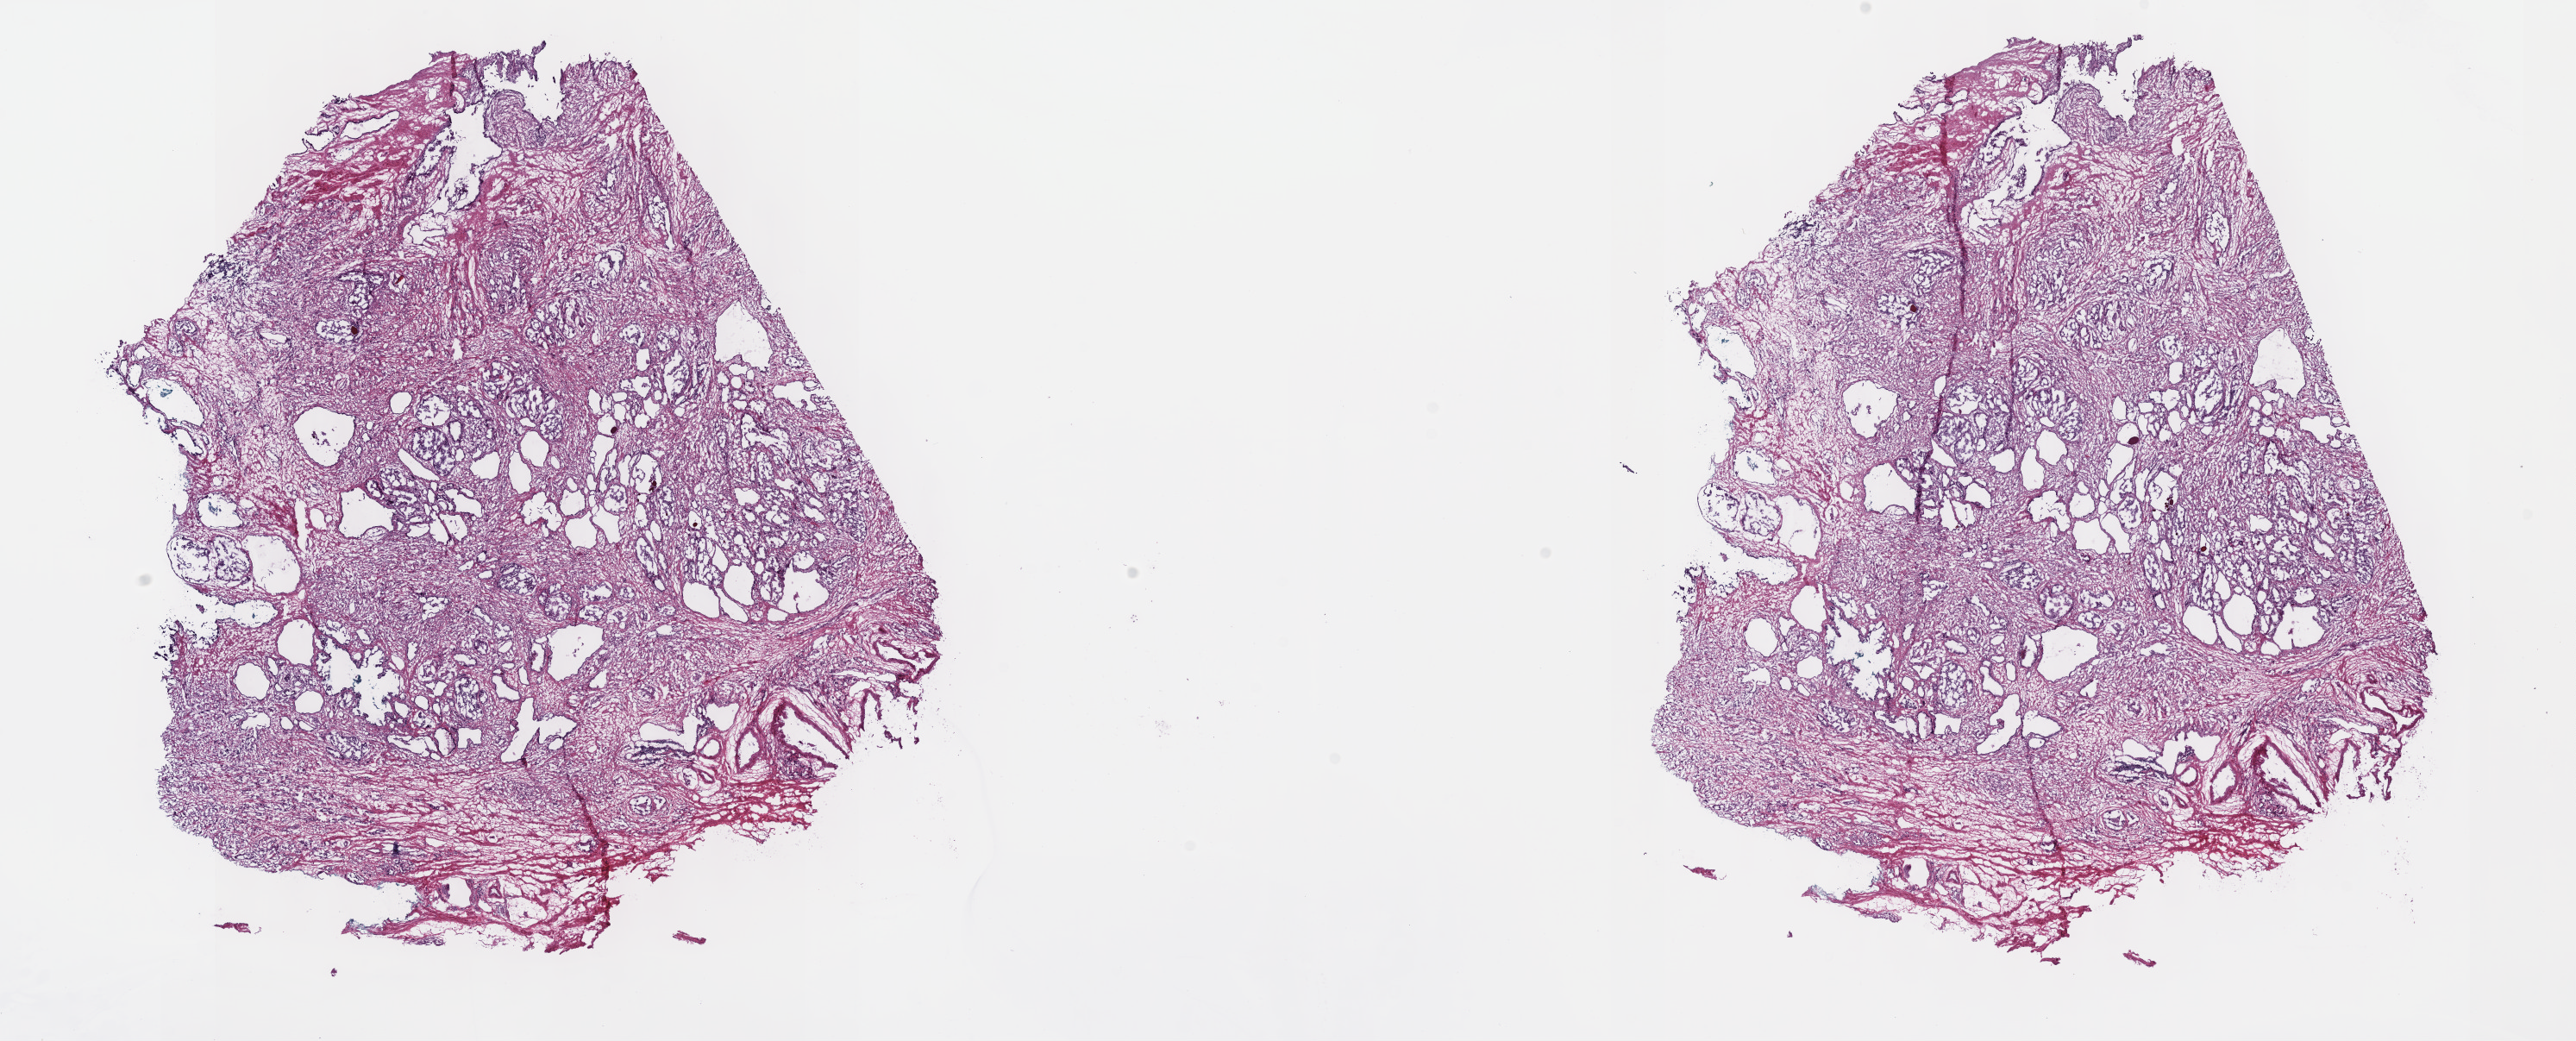
Whole-slide histology image, Hematoxylin and eosin (H&E) stained, whole scanned area (about 24.2 x 9.8 mm, slide scanned at 40x) shown as a low-resolution overview, frozen section from the top of the tissue portion, prostate, primary tumour sample. Male, age 65 years at initial diagnosis. Gleason score: 9 (4+5). Pathologist review of this section (percent, as recorded): tumour cells 60%, tumour nuclei 80%, normal cells 20%, stromal cells 20%, necrosis 0%. Infiltration values recorded for this section: lymphocyte infiltration 0%, monocyte infiltration 0%, neutrophil infiltration 0%.
Pathologic diagnosis: Adenocarcinoma, NOS (prostate gland).